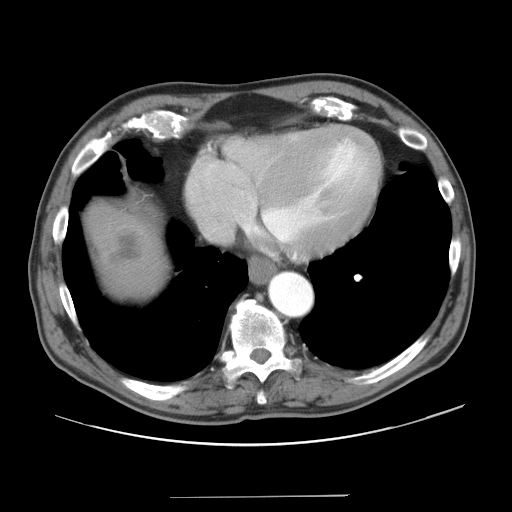
Contrast-enhanced abdominal CT, one axial slice. Slice 39 of 41 in the series (ordered by position). Reconstruction kernel STANDARD. Intravenous contrast given. Soft-tissue window (W 400 / L 40 HU). 512 × 512 image matrix, field of view 420 × 420 mm. Male patient, age 75 years. Case-level facts recorded for this patient, not image findings: diagnosis: colorectal cancer liver metastases, imaged before liver resection; multiple liver metastases: no; largest metastasis: 5.2 cm.
Annotated regions visible in this slice (expert manual segmentation):
- liver: box from (x=91, y=206) to (x=165, y=295) px
- liver metastasis: (x=111, y=236)–(x=141, y=262)